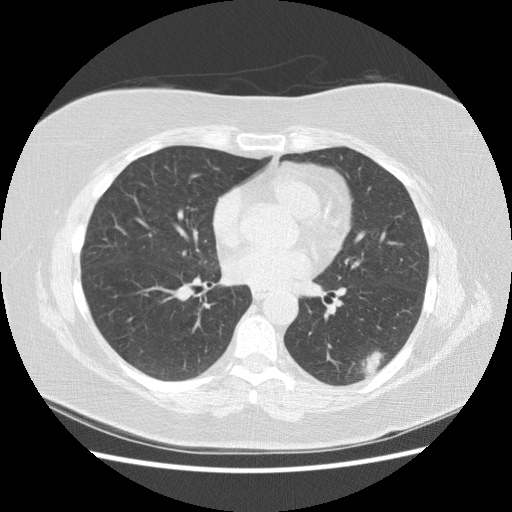
Low-dose screening chest CT, one axial slice. Position 74 of 151 along the scan axis. 120 kVp. Lung window (W 1500 / L -600 HU). 512 × 512 image matrix, field of view 360 × 360 mm.
Structures marked on this image (outlined manually by an expert reader):
- lesion 1 (tumor, lower lobe of left lung): bounding box <360,350,384,378> (left, top, right, bottom; pixels)